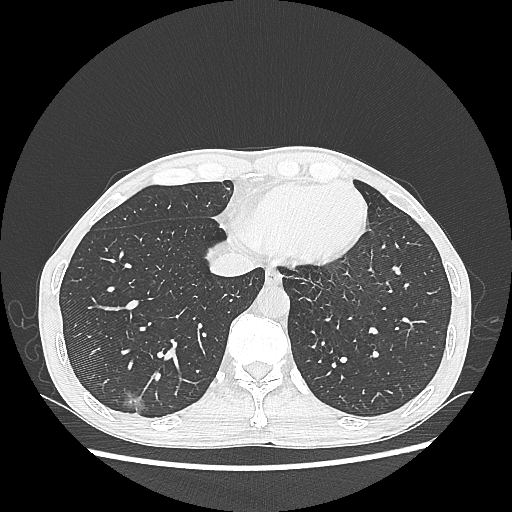
Chest CT, one axial slice. Position 74 of 270 along the scan axis. Lung window (W 1500 / L -600 HU). 512 × 512 image matrix, field of view 360 × 360 mm. Male patient, age 60 years. From the clinical record (not read from this slice): clinical TNM (as recorded): T1c N0 M0; histopathological grade: G2.
Annotated regions visible in this slice (bounding box drawn by a radiologist):
- lung tumour (recorded histology: adenocarcinoma): bounding box <119,386,147,424> (left, top, right, bottom; pixels)